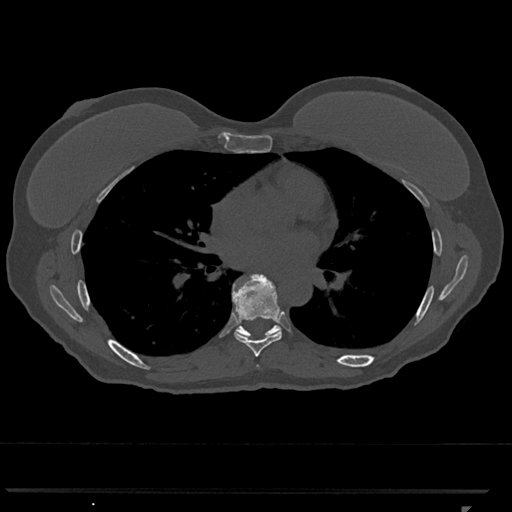
CT including the spine, one axial slice. Slice 699 of 793 in the series (ordered by position). 120 kVp. Bone window (W 1800 / L 400 HU). 0.5 mm slice thickness. 512 × 512 image matrix, field of view 380 × 380 mm. Female patient, age 62 years. From the clinical record (not read from this slice): primary cancer: renal.
Annotated regions visible in this slice (semi-automatic segmentation, software-assisted and operator-edited):
- T7 vertebra: bounding box (x1, y1, x2, y2) in pixels: (232, 275, 282, 357)
- T8 vertebra: (233, 286, 280, 337)